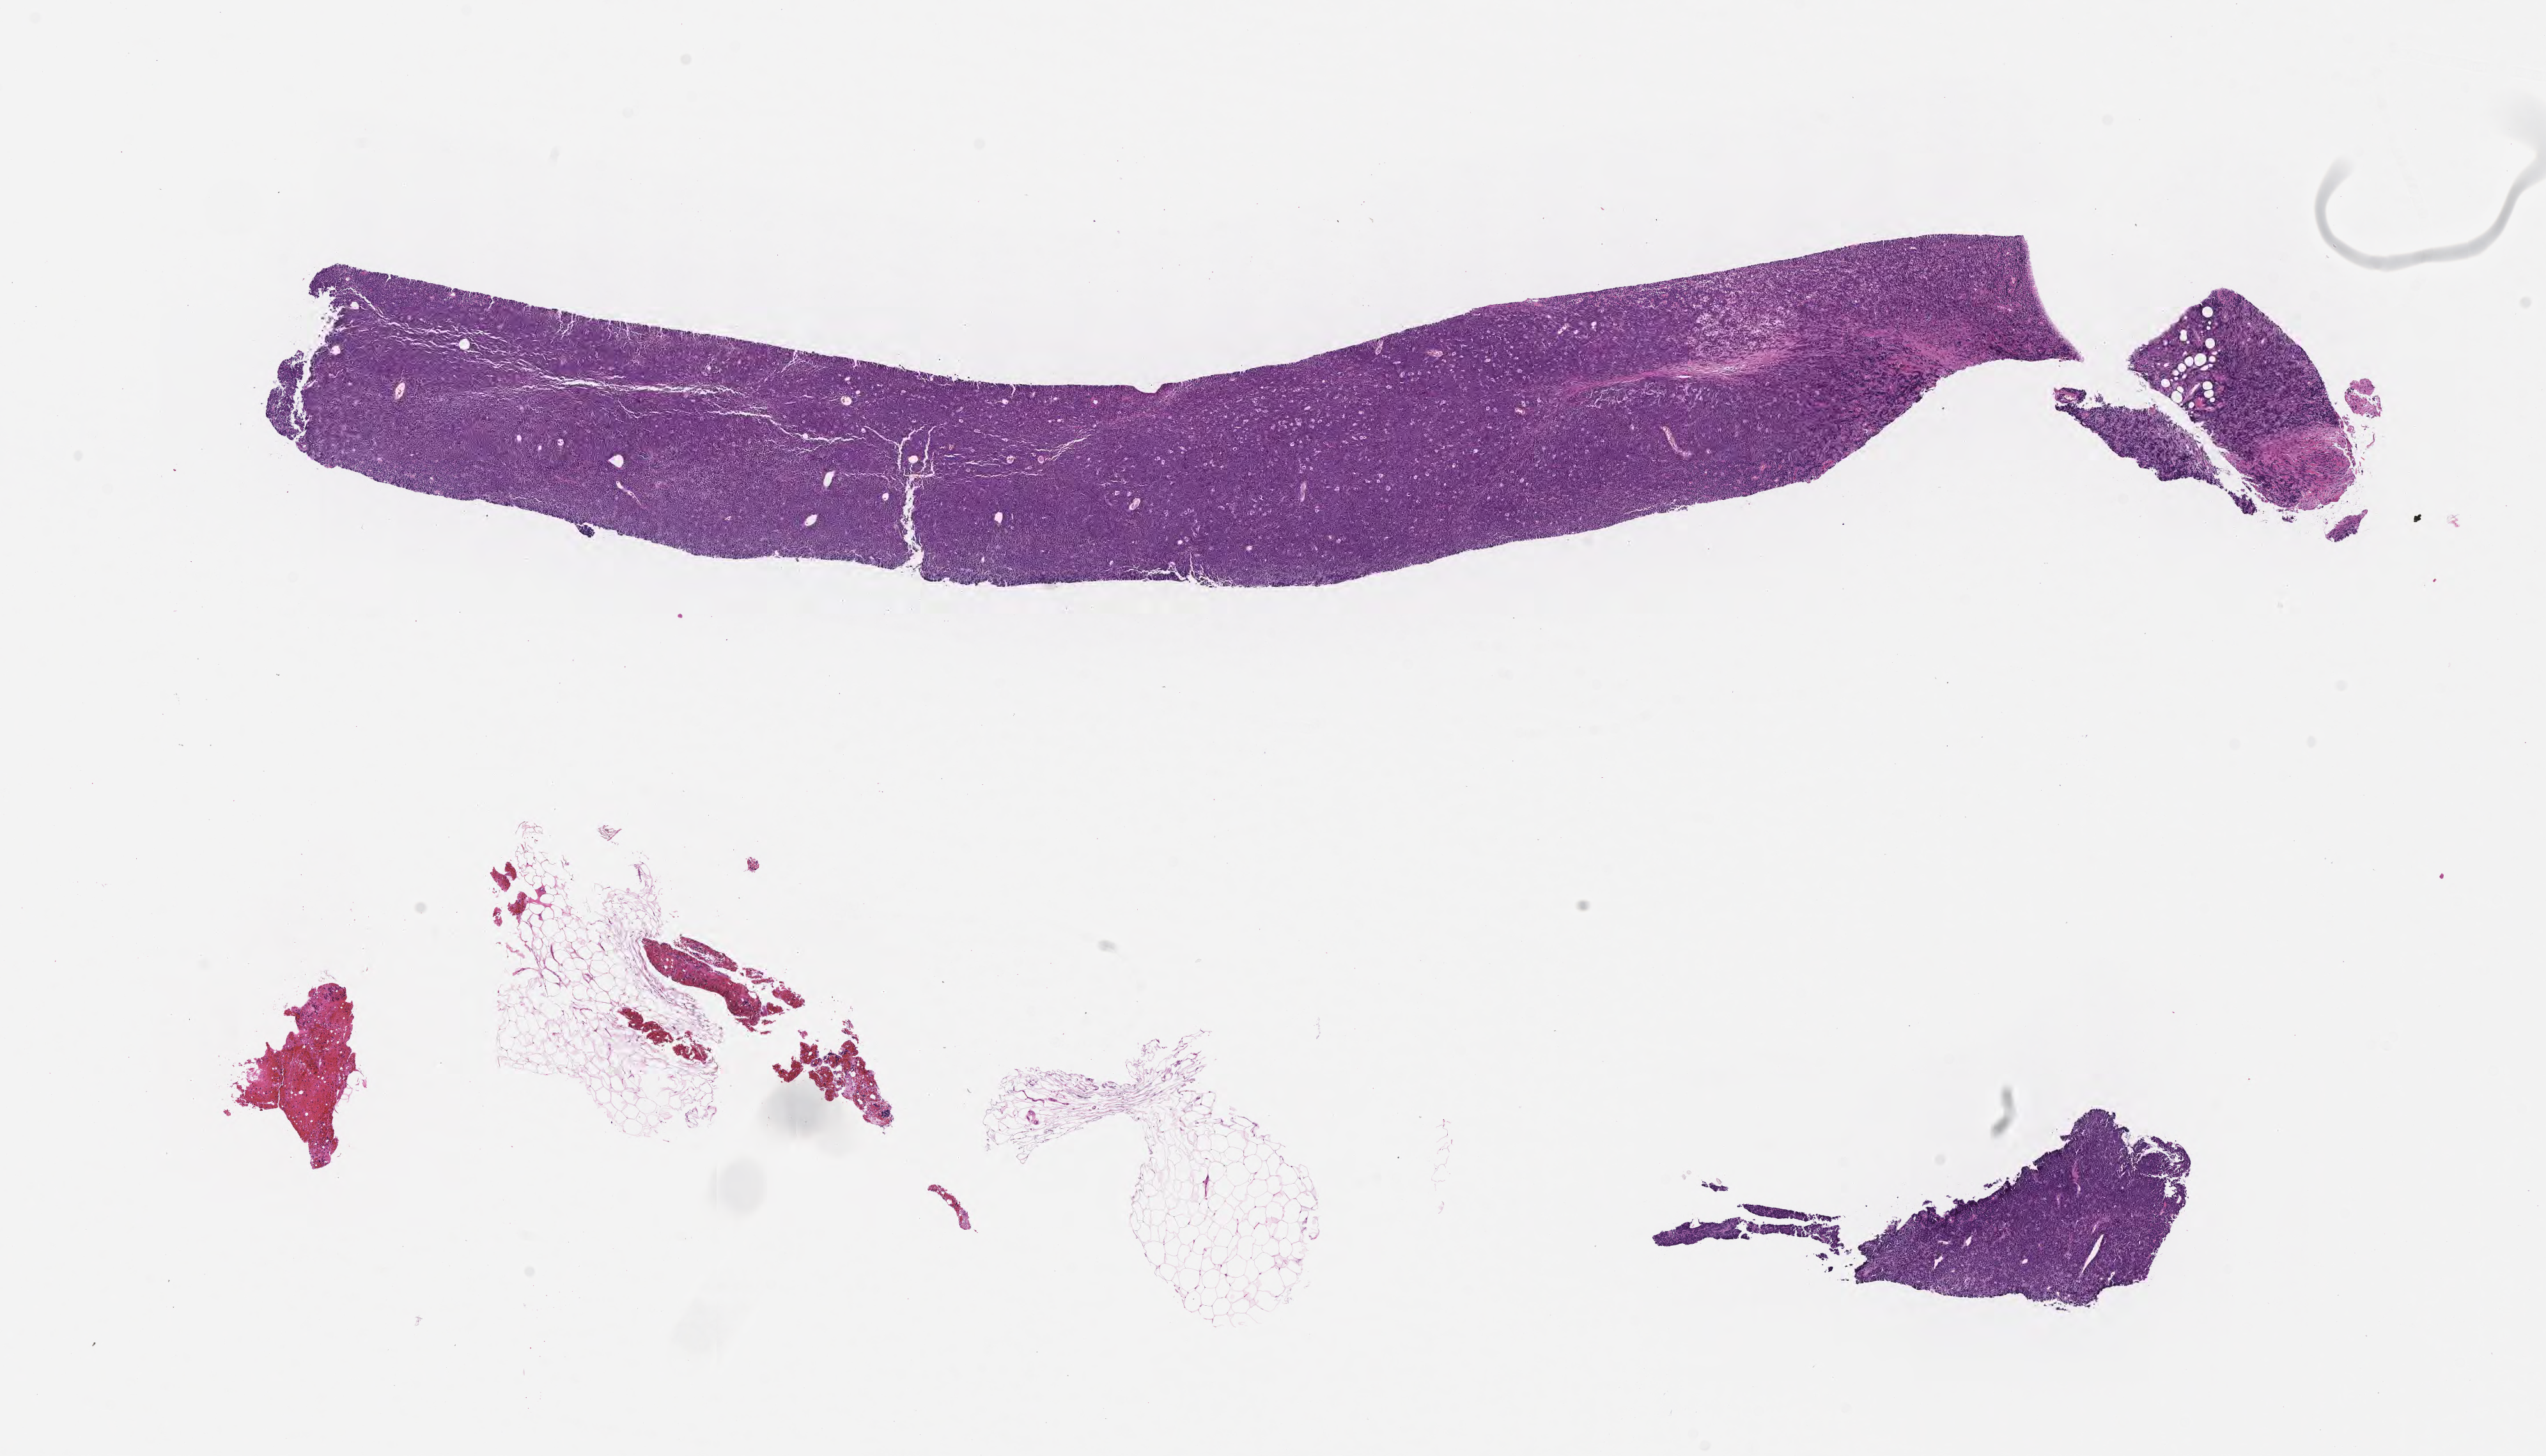
Whole-slide image, H&E stain — low-resolution overview of the scanned area, about 16.1 x 9.2 mm. FFPE section. Primary tumor. Patient female; 61 years old. Pathologist review of this section (percent, as recorded): tumor cells 90%, tumor nuclei 95%, stromal cells 10%, necrosis 0%, normal cells 0%. Inflammatory infiltration, as recorded: lymphocyte infiltration 40%, monocyte infiltration 20%, neutrophil infiltration 5%.
* Ann Arbor stage (patient): Stage IV
* histologic diagnosis: Burkitt lymphoma, NOS